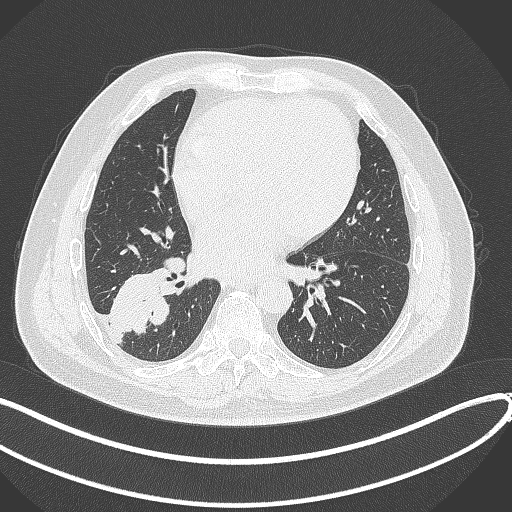
Chest CT, one axial slice. Slice 152 of 360 in the series (ordered by position). Reconstruction kernel B70f. 120 kVp. Lung window (W 1500 / L -600 HU). 1 mm slice thickness. 512 × 512 image matrix, field of view 400 × 400 mm. Male patient, age 59 years.
Structures marked on this image (rectangle marked by the reading radiologist):
- lung tumour (recorded histology: adenocarcinoma): bounding box [x1, y1, x2, y2] px = [106, 272, 173, 338]